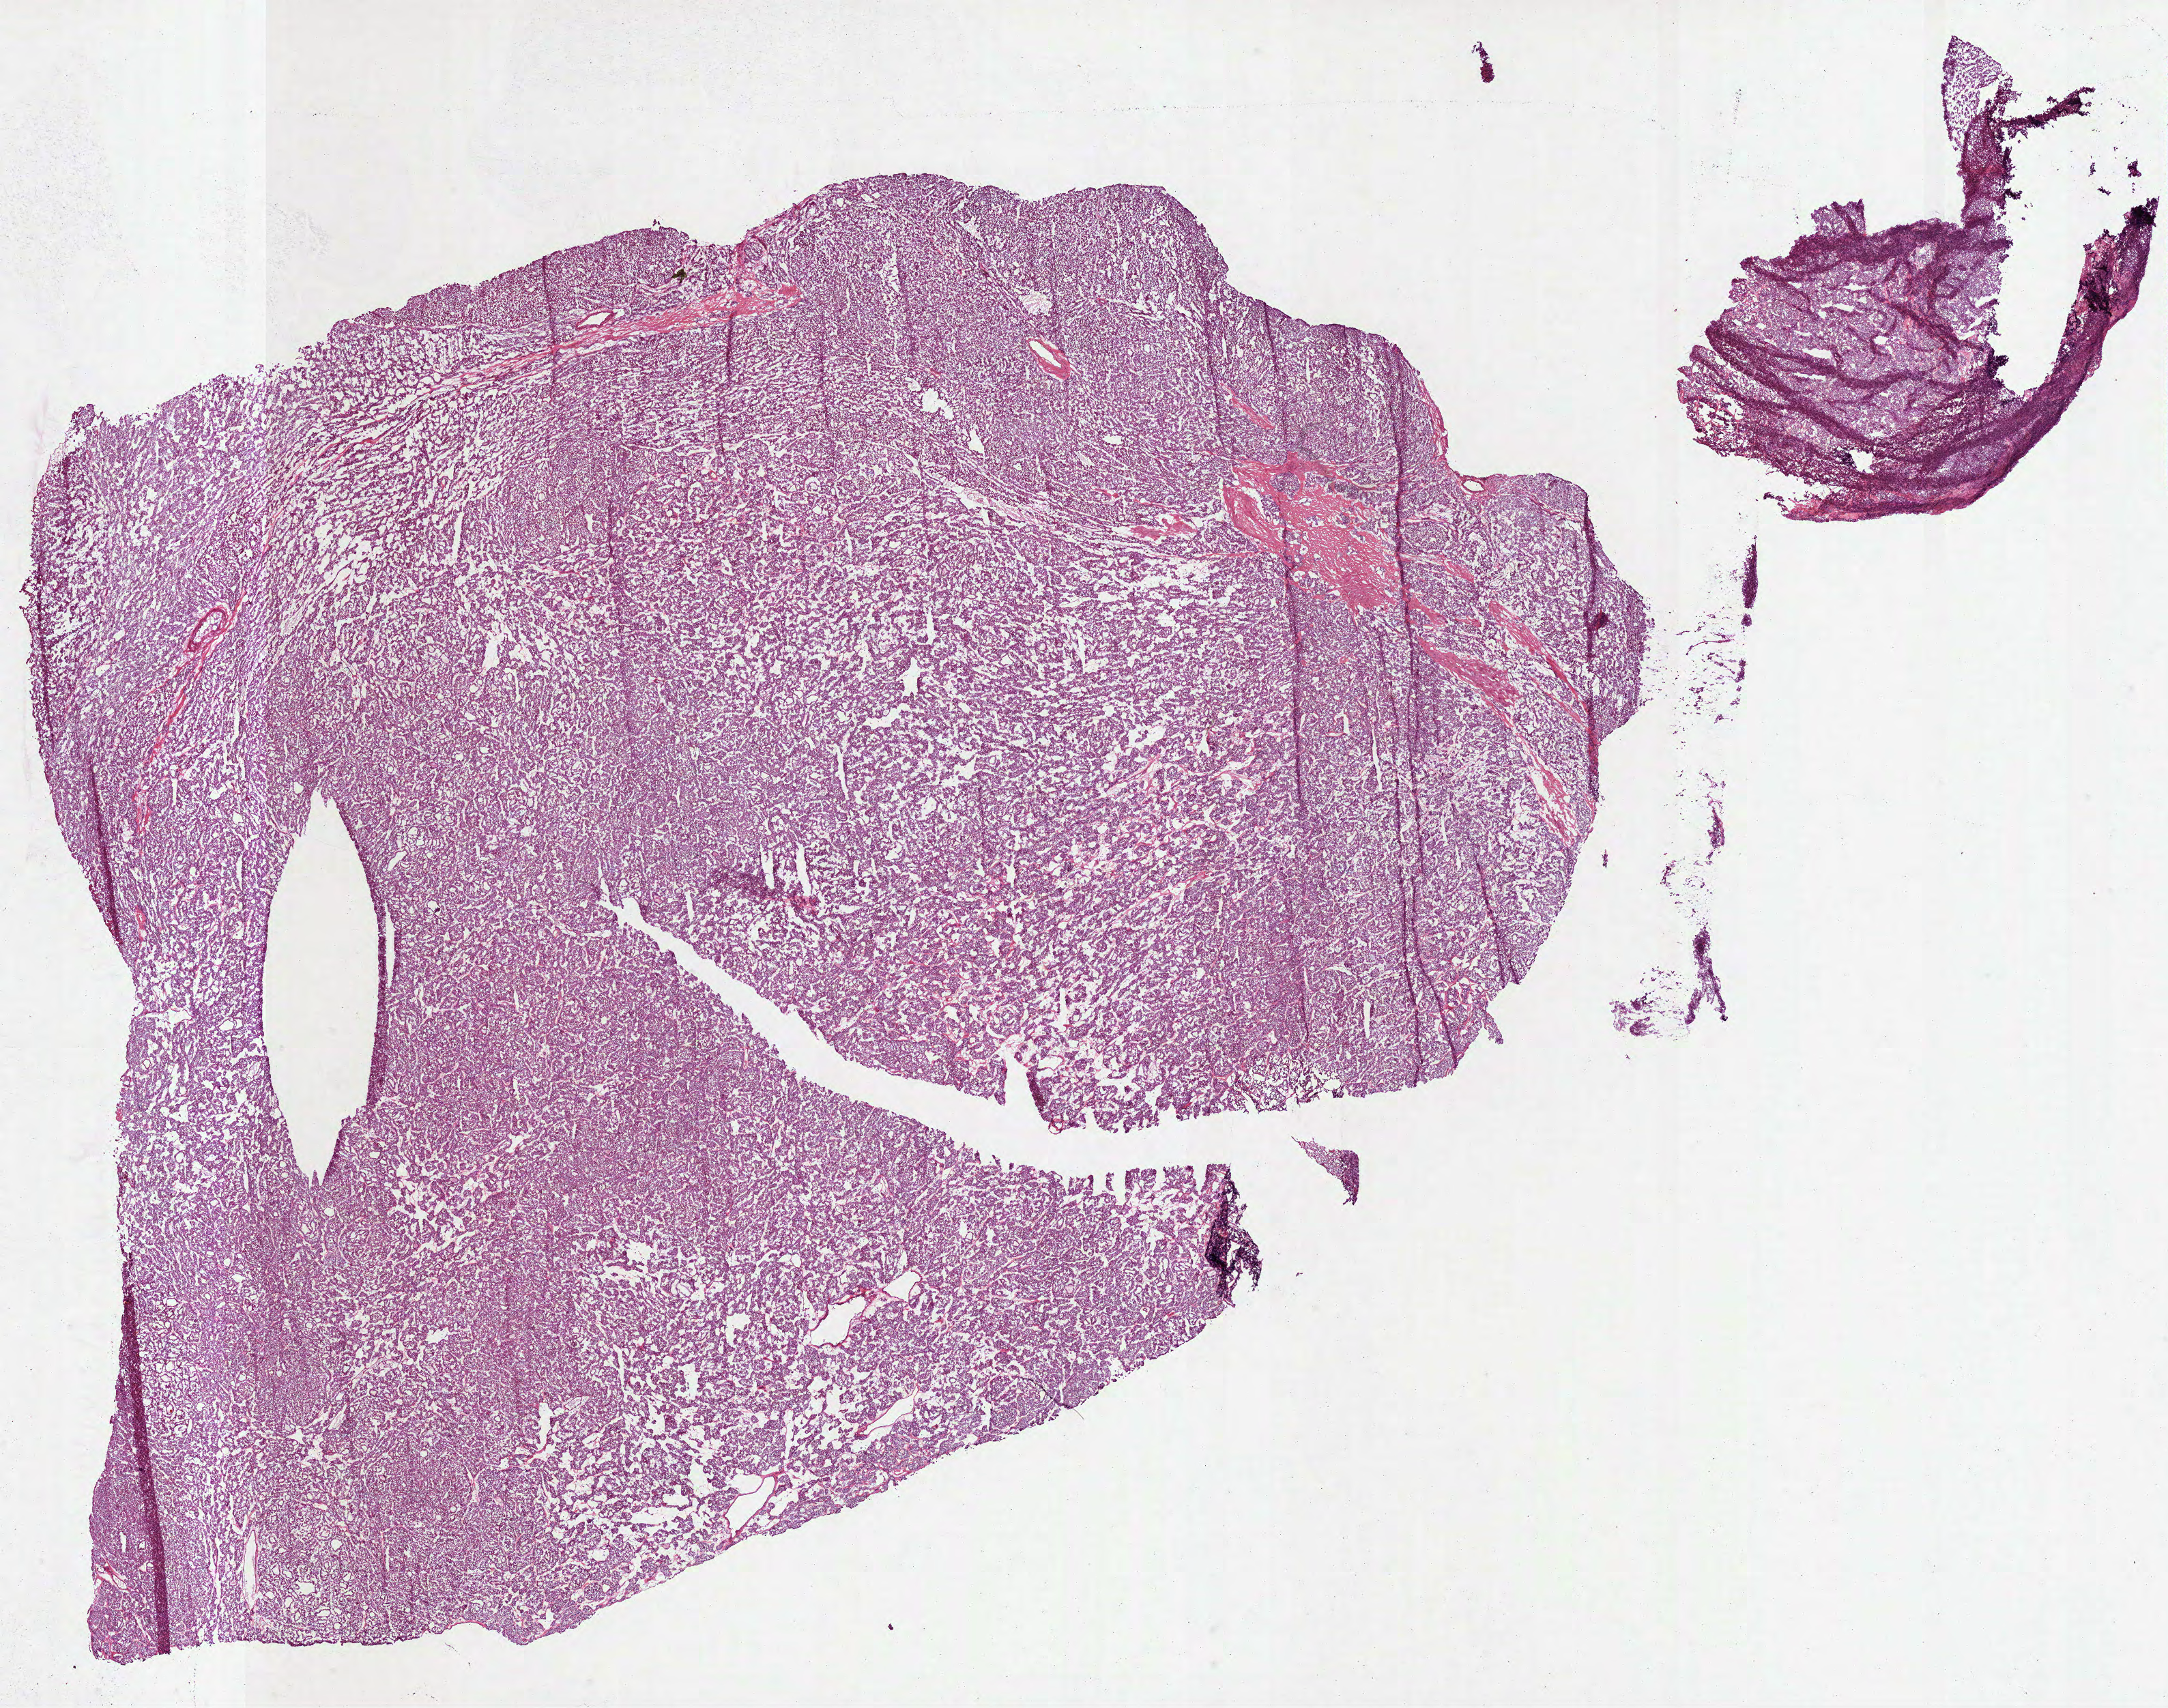
Digitized H&E-stained tissue section (whole slide), a low-resolution overview of the entire scanned area, about 25.6 x 20.2 mm (from a 40x scan); frozen section from the bottom of the tissue portion; primary tumour sample from the kidney. Male patient; age at initial diagnosis 44 years. Composition of this section per pathologist review: tumour cells 100%, tumour nuclei 90%, normal cells 0%, stromal cells 0%, necrosis 0%. Inflammatory infiltration, as recorded: lymphocyte infiltration 0%, monocyte infiltration 0%, neutrophil infiltration 0%.
TNM: T1b N0. AJCC pathologic stage: I (6th edition). Diagnosis: Renal cell carcinoma, chromophobe type. Lymph nodes positive (case pathology): 0 of 6 examined.